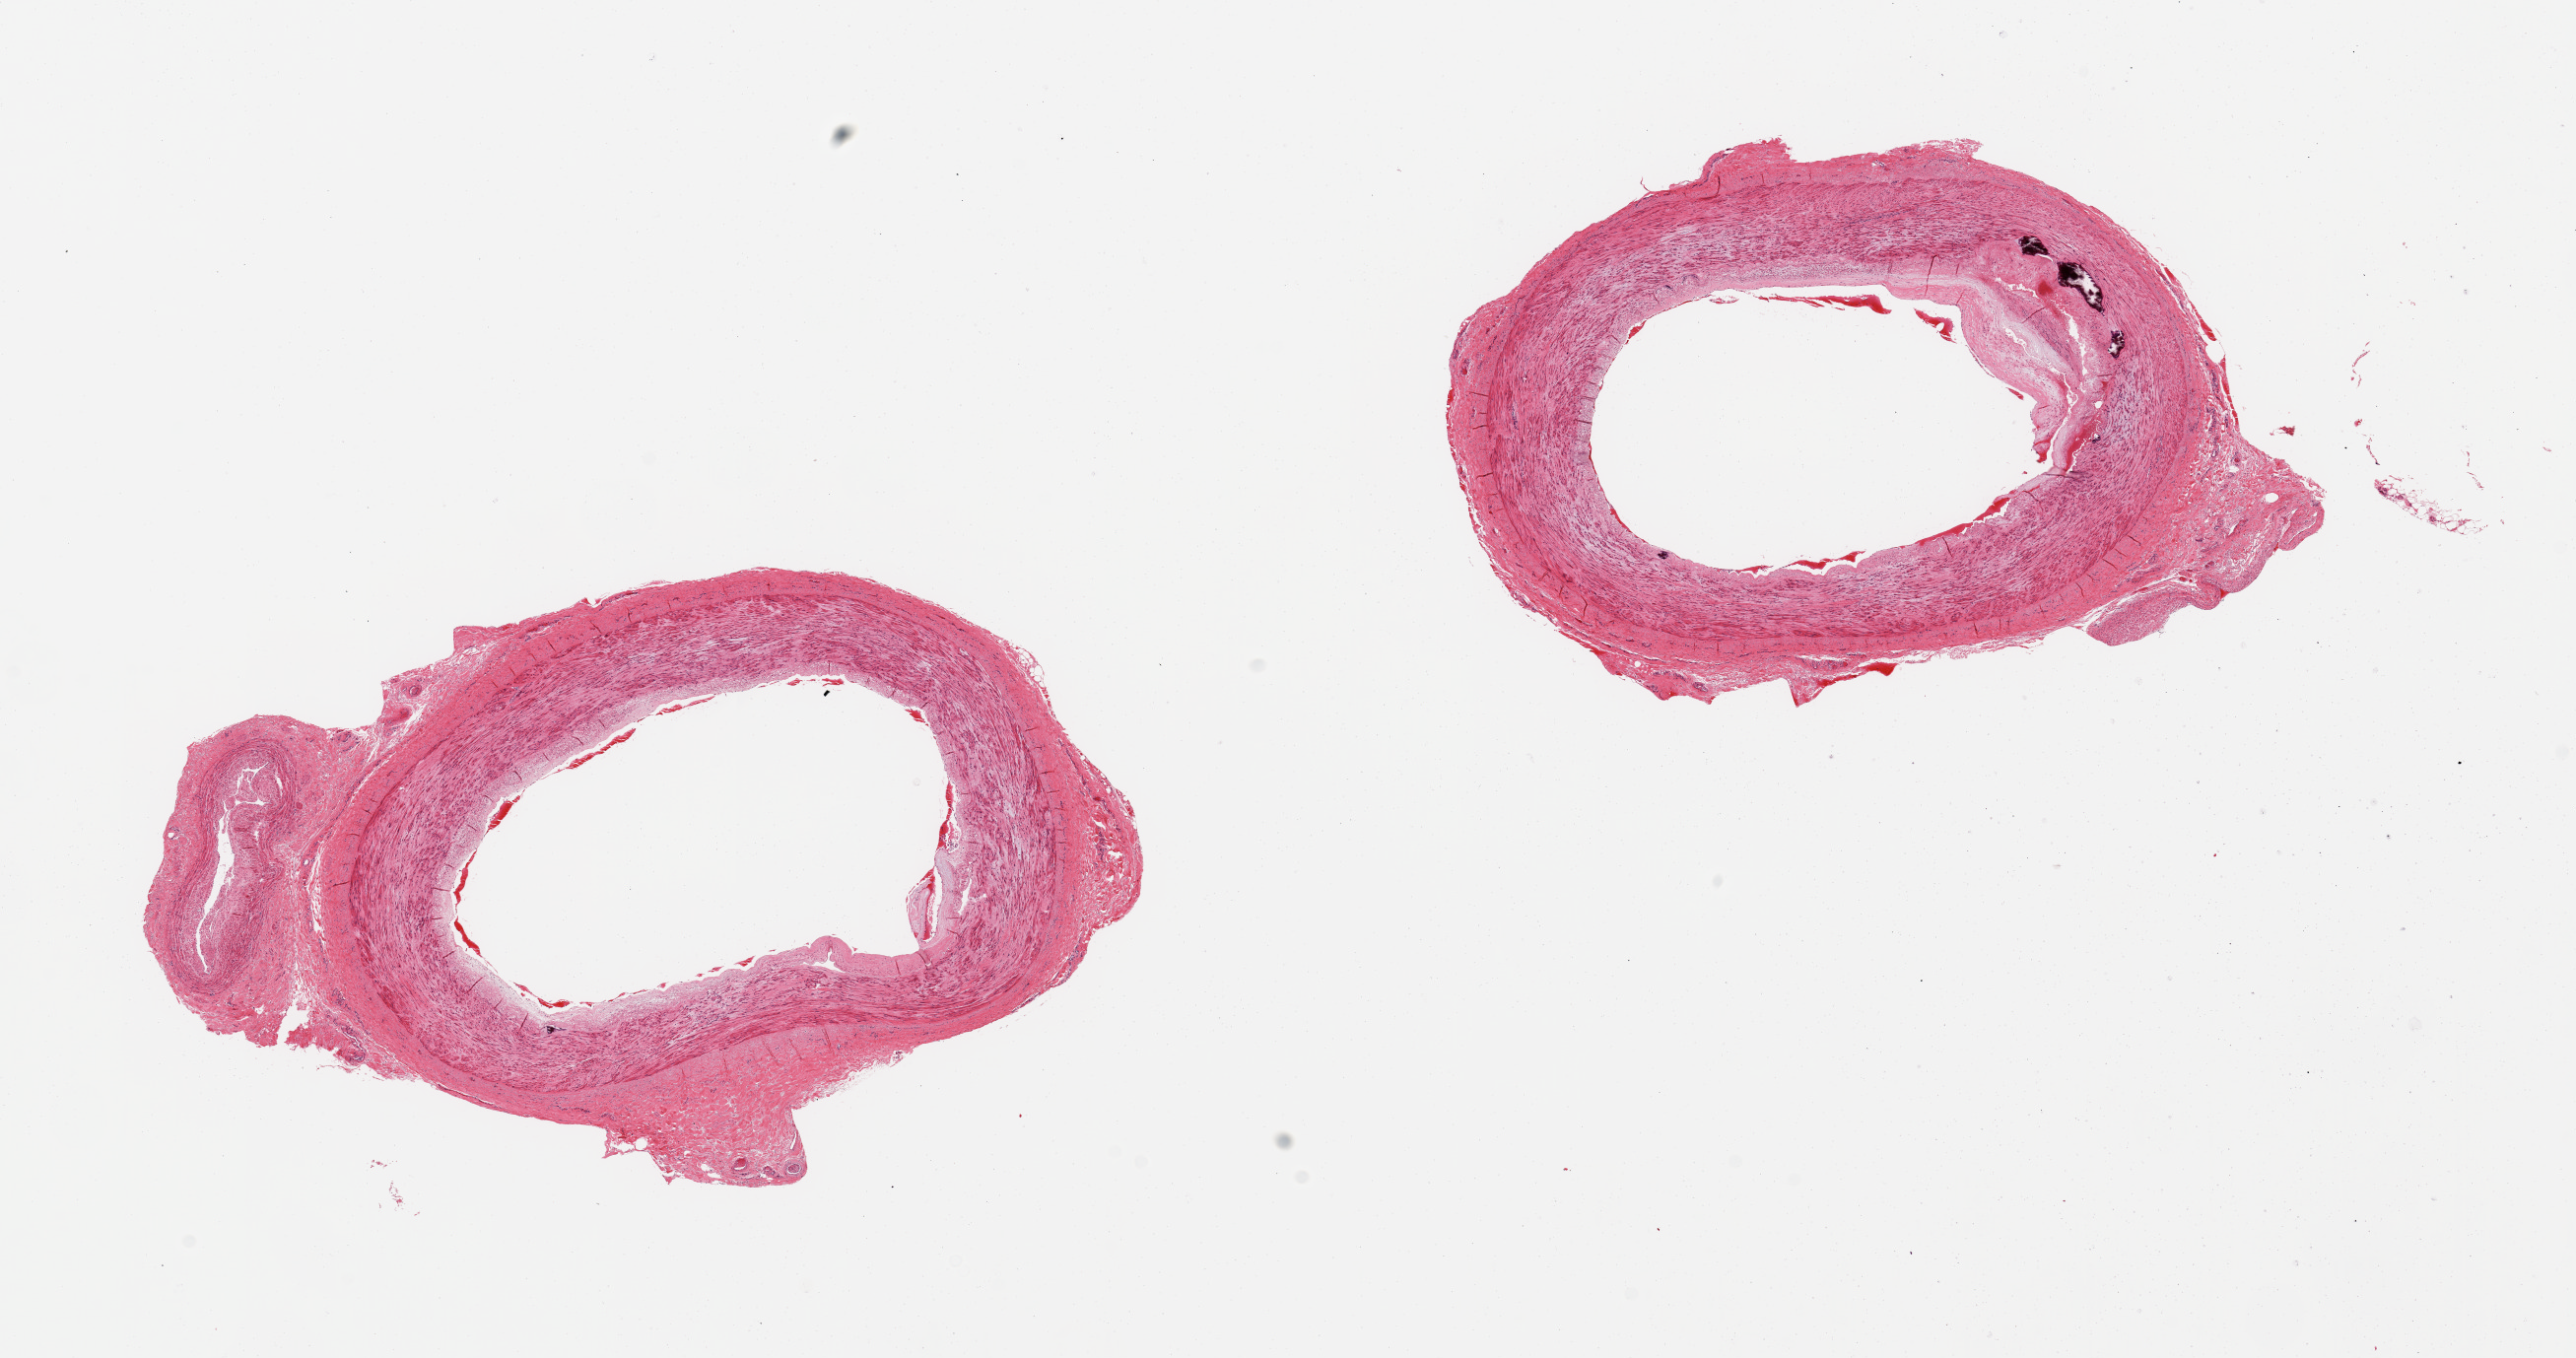
Whole-slide image, H&E stain, low-resolution overview of the scanned area, about 20.7 x 10.9 mm (slide scanned at 20x); PAXgene-fixed, paraffin-embedded tissue; target tissue: tibial artery; tissue donor sample. Donor sex: male.
• pathologist's review note for this sample: 2 pieces; focal plaques and calcium deposits; well trimmed of external fat